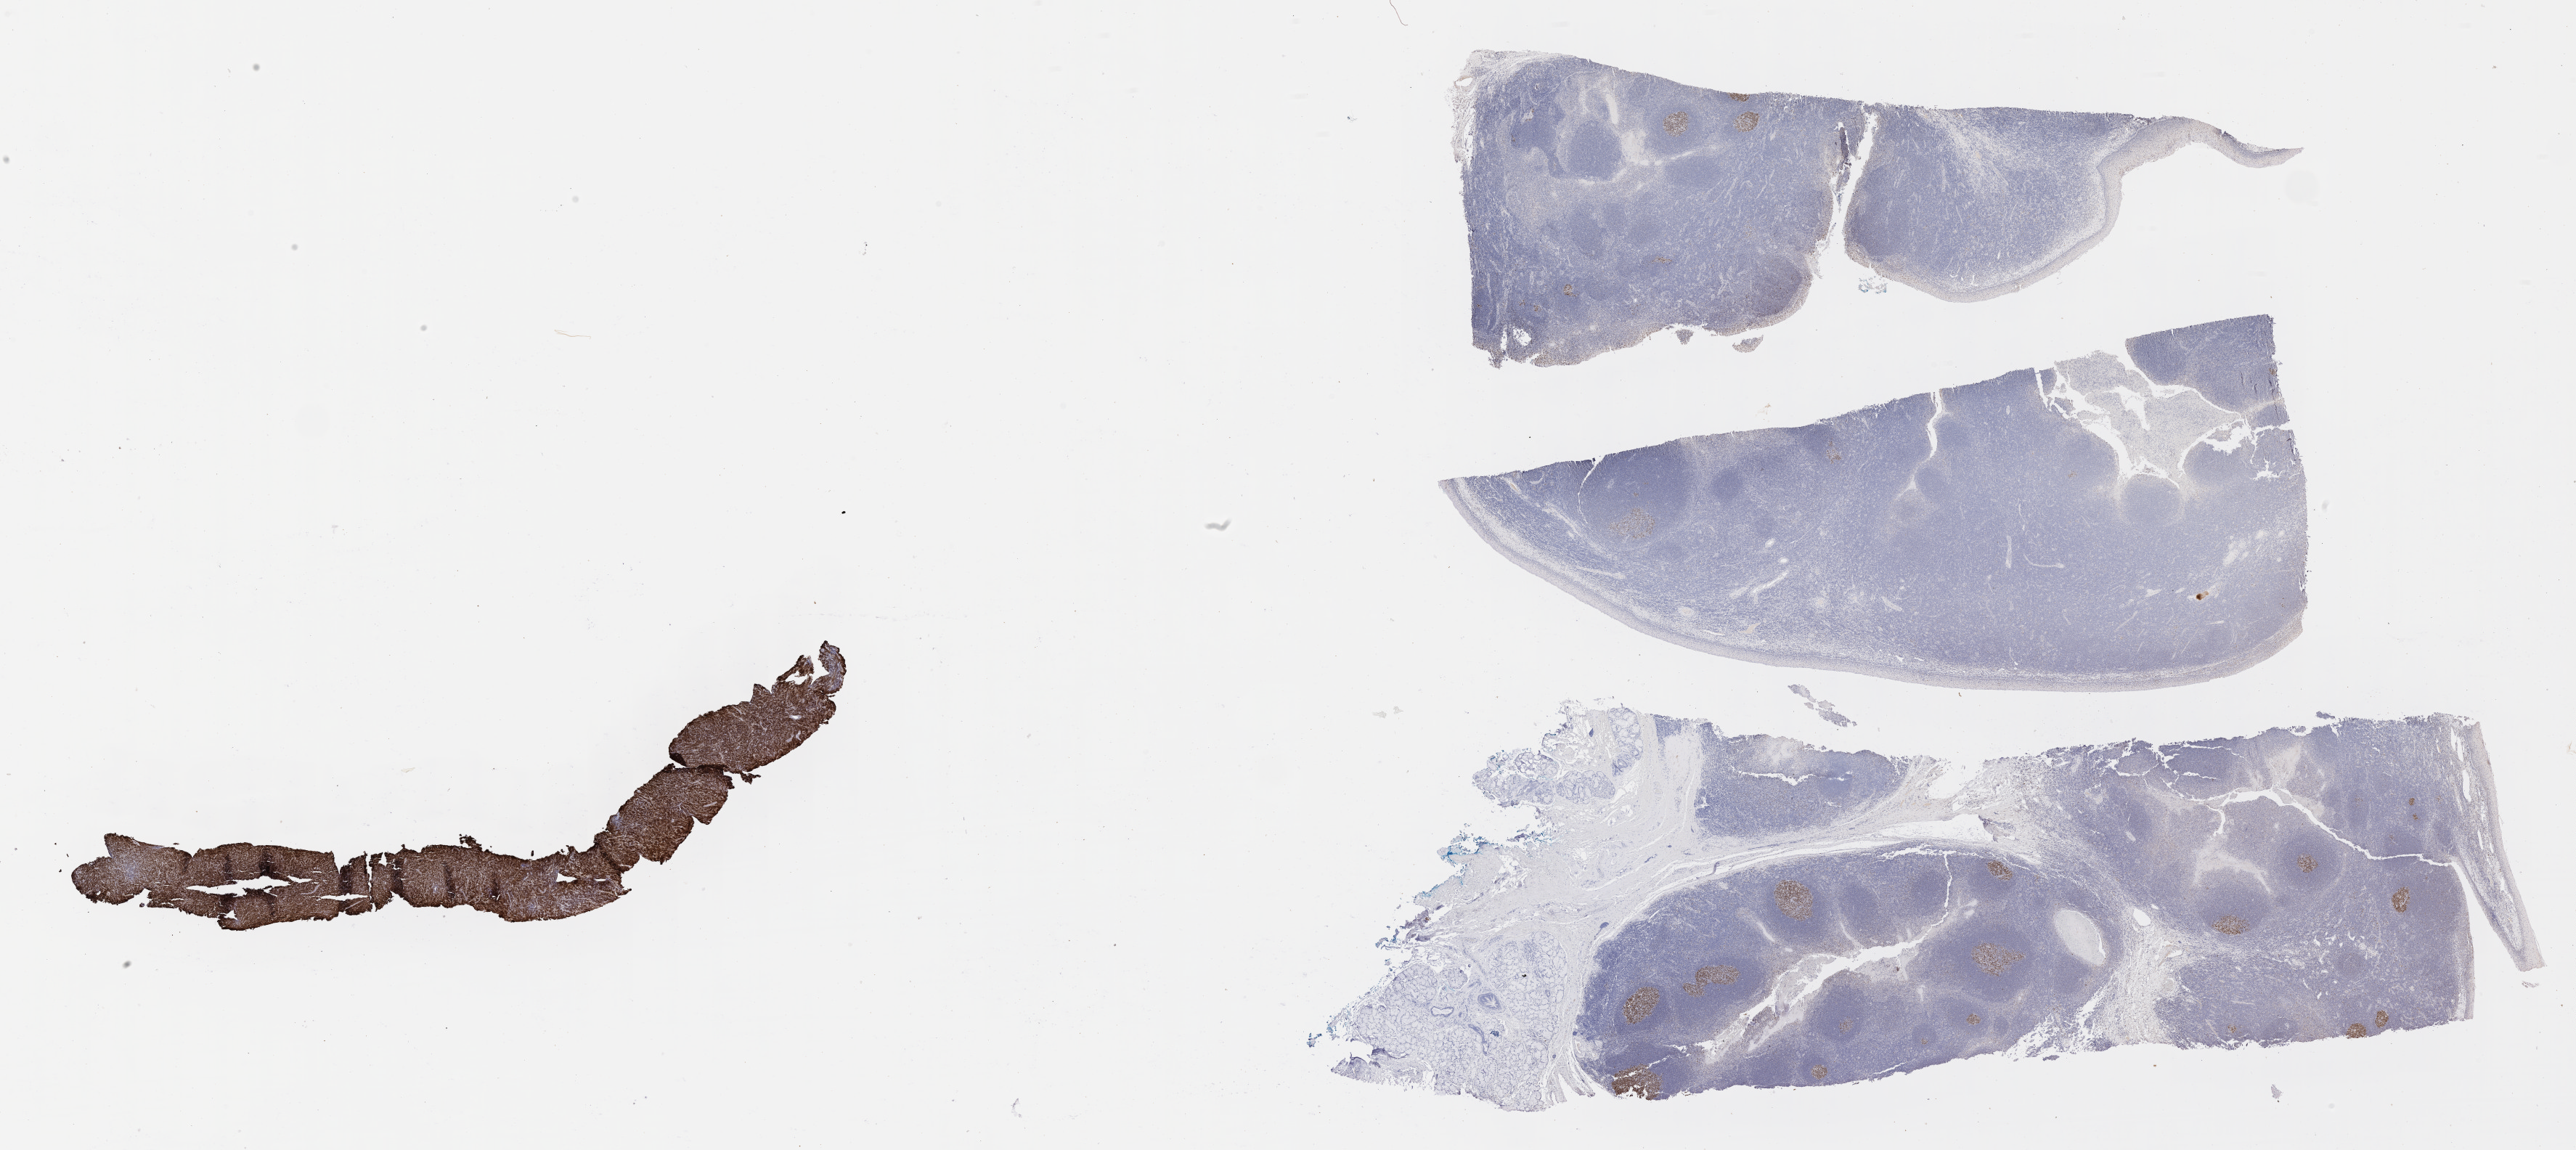
Immunohistochemistry (IHC) whole-slide image stained for BCL6, low-resolution overview of the scanned area, about 28.7 x 12.8 mm. Specimen: tumor tissue. Anatomic site: kidney. Male, age 9 years at initial diagnosis.
- diagnosis: Burkitt lymphoma, NOS